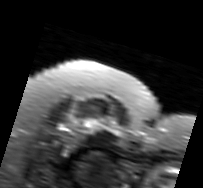
MRI of an extremity soft-tissue mass, one axial slice; position 67 of 91 along the scan axis; T2-weighted fat-saturated; MR volume resampled by the dataset authors to the PET/CT grid (not the native acquisition matrix); 3.27 mm slice thickness; 203 × 188 image matrix, field of view 198 × 184 mm. Female patient. Case-level facts recorded for this patient, not image findings: histological type: malignant solitary fibrous tumor; grade: intermediate; site of the primary tumour: right thigh.
Annotated regions visible in this slice (expert contour drawn on MRI and transferred to this co-registered scan by the dataset authors):
- gross tumour volume including surrounding oedema: bounding box <62,115,121,148> (left, top, right, bottom; pixels)